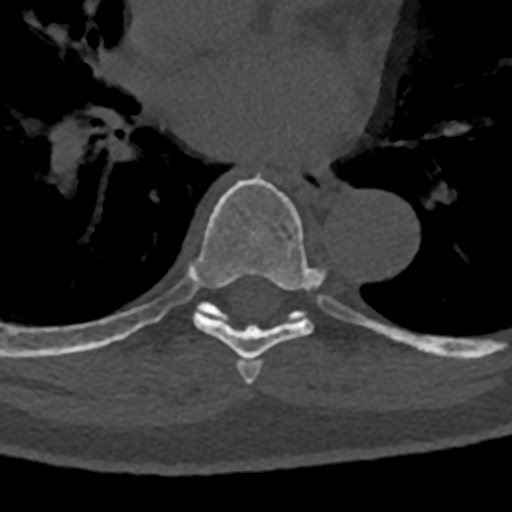
CT including the spine, one axial slice. Position 753 of 797 along the scan axis. Reconstruction kernel Br40s/3. 120 kVp. Bone window (W 1800 / L 400 HU). 0.5 mm slice thickness. 512 × 512 image matrix, field of view 160 × 160 mm. Male patient, age 74 years. Case-level facts recorded for this patient, not image findings: primary cancer: renal; vertebrae with lytic lesions (as recorded): T10, L1, L2, L3, L4, L5.
Annotated regions visible in this slice (semi-automatically segmented with operator editing):
- T6 vertebra: bounding box [x1, y1, x2, y2] px = [237, 360, 262, 385]
- T7 vertebra: [71, 177, 366, 365]
- T8 vertebra: [70, 303, 432, 355]